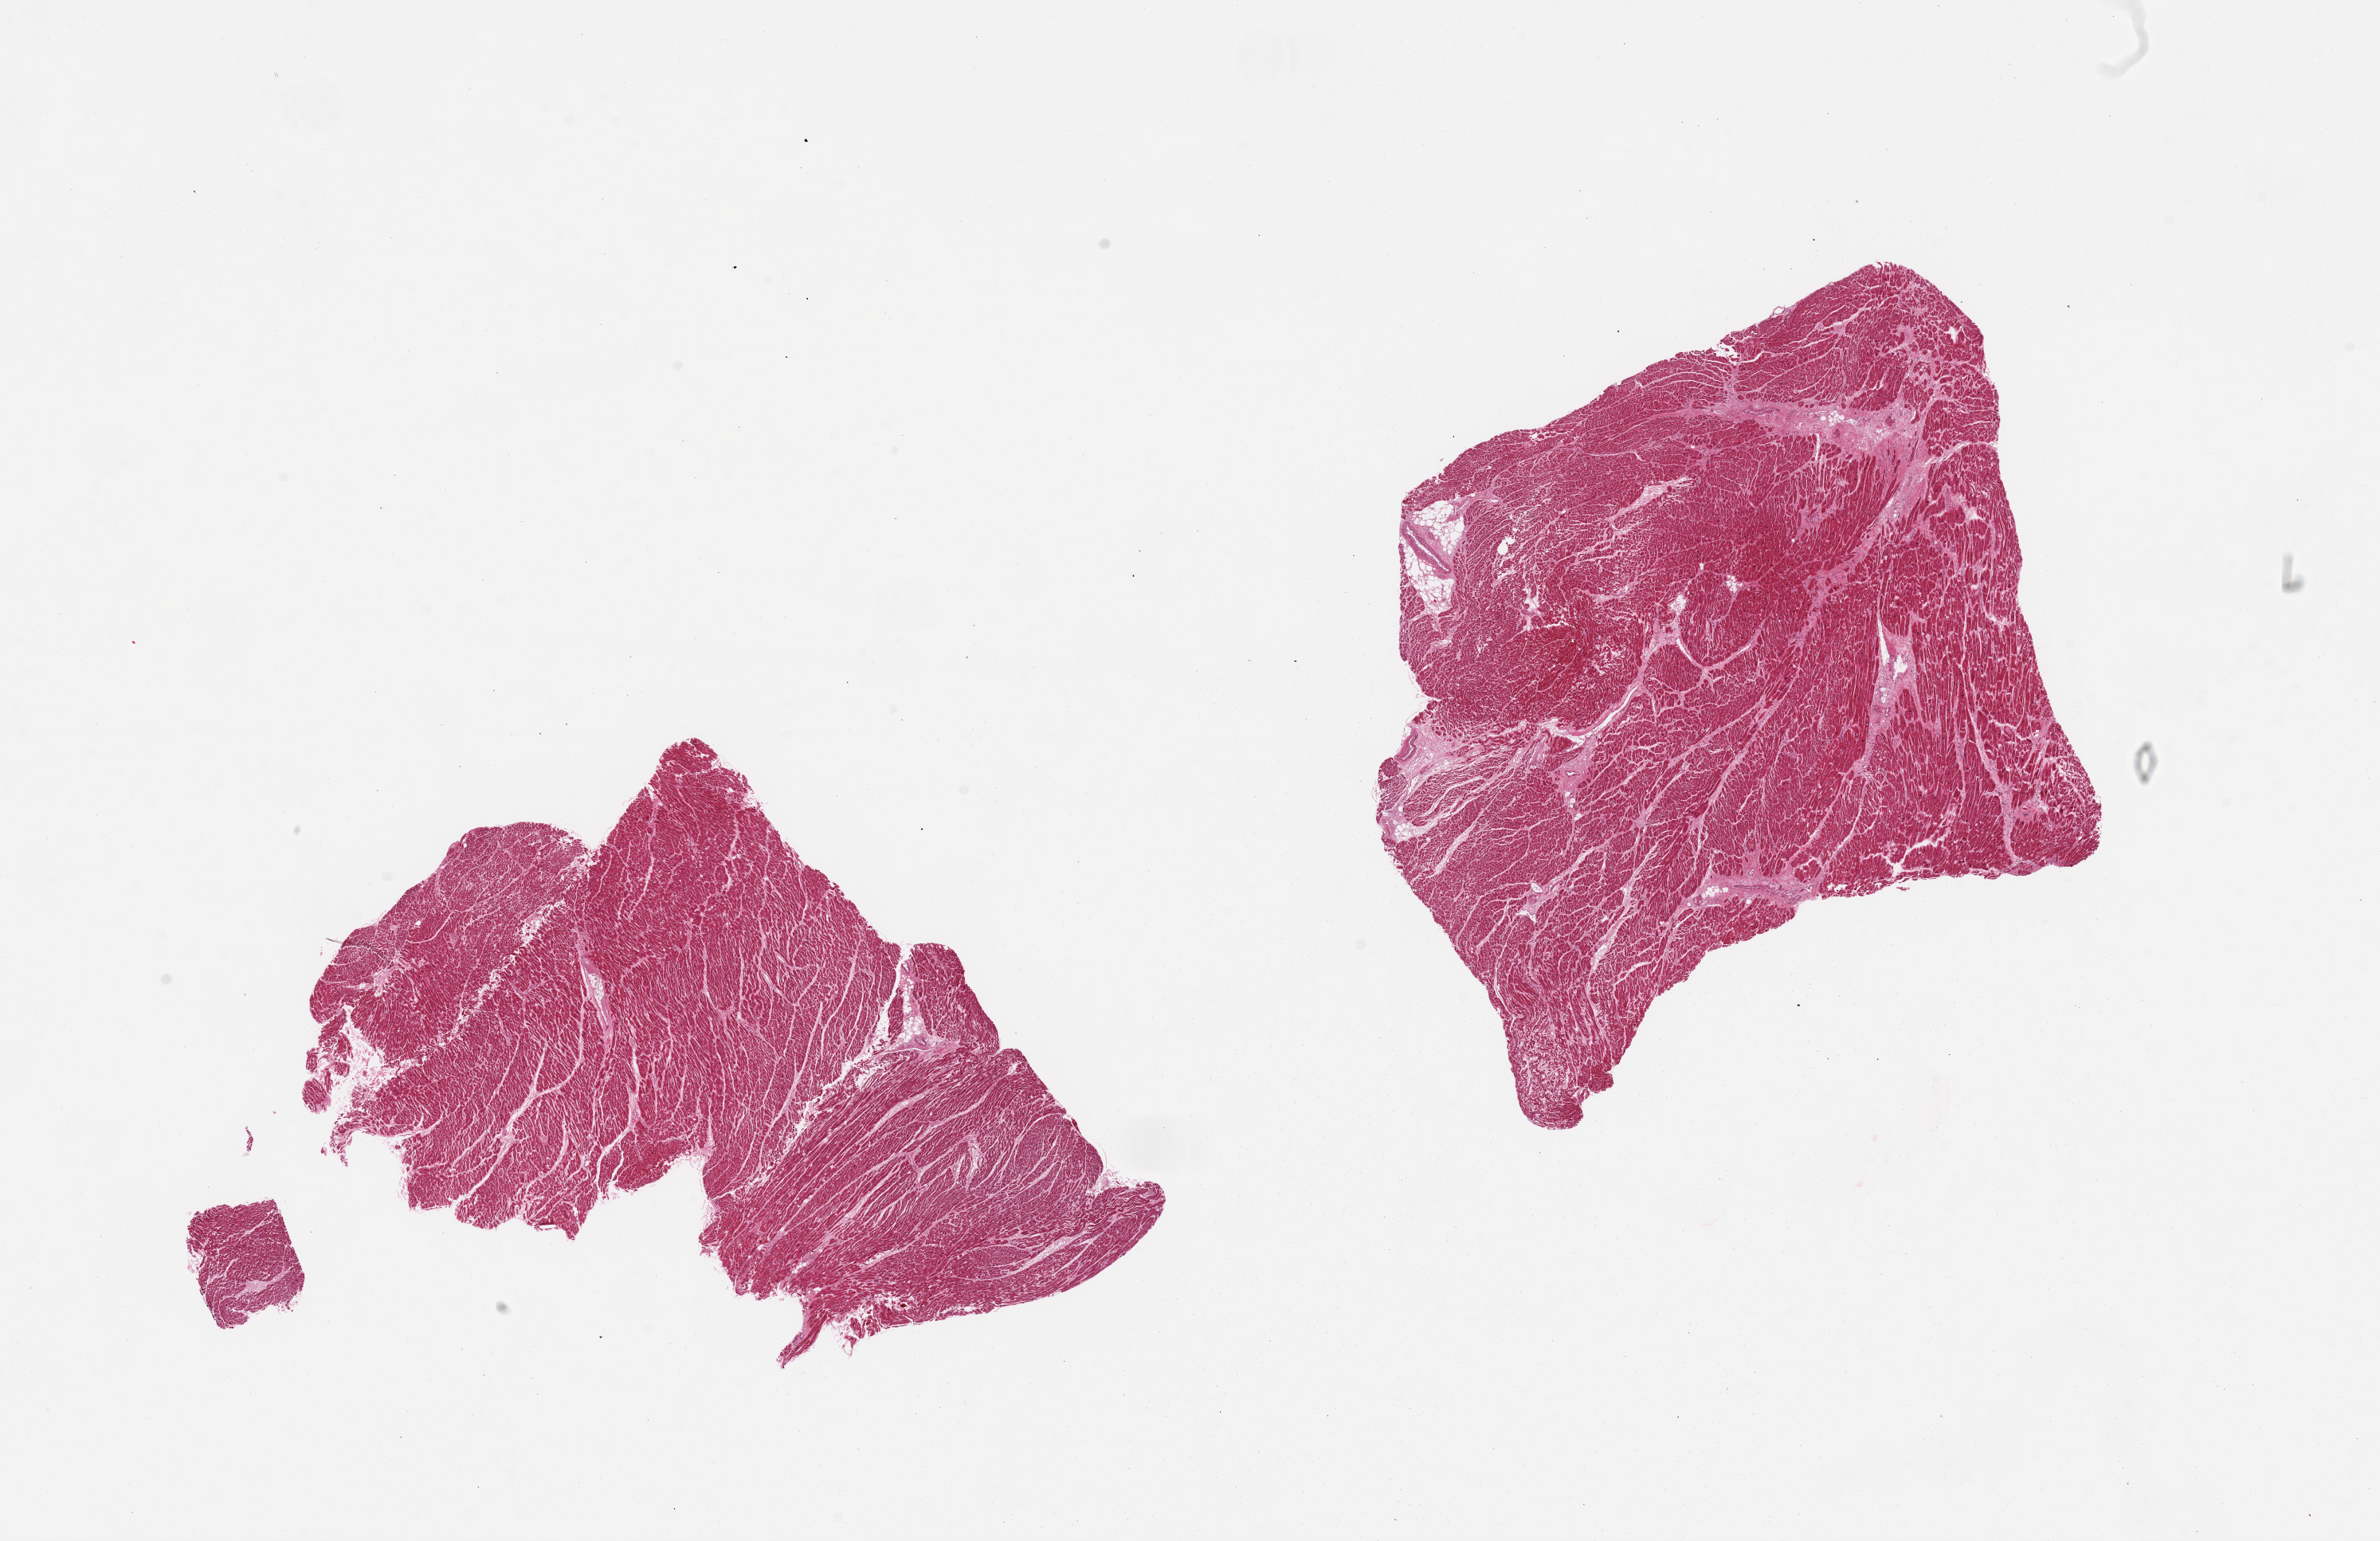
Whole-slide image, hematoxylin and eosin (H&E) stain, brightfield — a low-resolution overview of the entire scanned area, about 23.6 x 15.3 mm (slide scanned at 20x), PAXgene-fixed paraffin-embedded (PFPE) section, target tissue: heart, donor tissue sample. Female donor.
Pathologist's review note for this sample: 2 pieces; patchy fibrosis <10%, hypertrophic fibers.